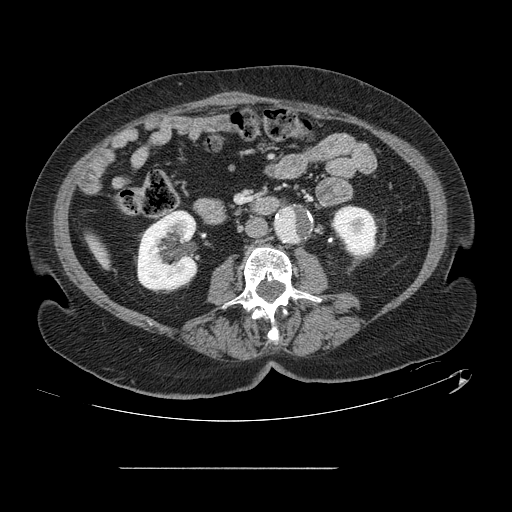
Contrast-enhanced abdominal CT, one axial slice. 120 kVp. Intravenous contrast given. Soft-tissue window (W 400 / L 40 HU). 2.5 mm slice thickness. 512 × 512 image matrix. Female patient, age 75 years. Case-level facts recorded for this patient, not image findings: diagnosis: colorectal cancer liver metastases, imaged before liver resection; multiple liver metastases: no; largest metastasis: 2.4 cm; disease in both lobes: no.
Outlined on this slice (outlined manually by an expert reader):
- liver: bounding box (x1, y1, x2, y2) in pixels: (97, 247, 108, 264)
- planned liver remnant (the part of the liver to remain after resection): (96, 246, 105, 259)